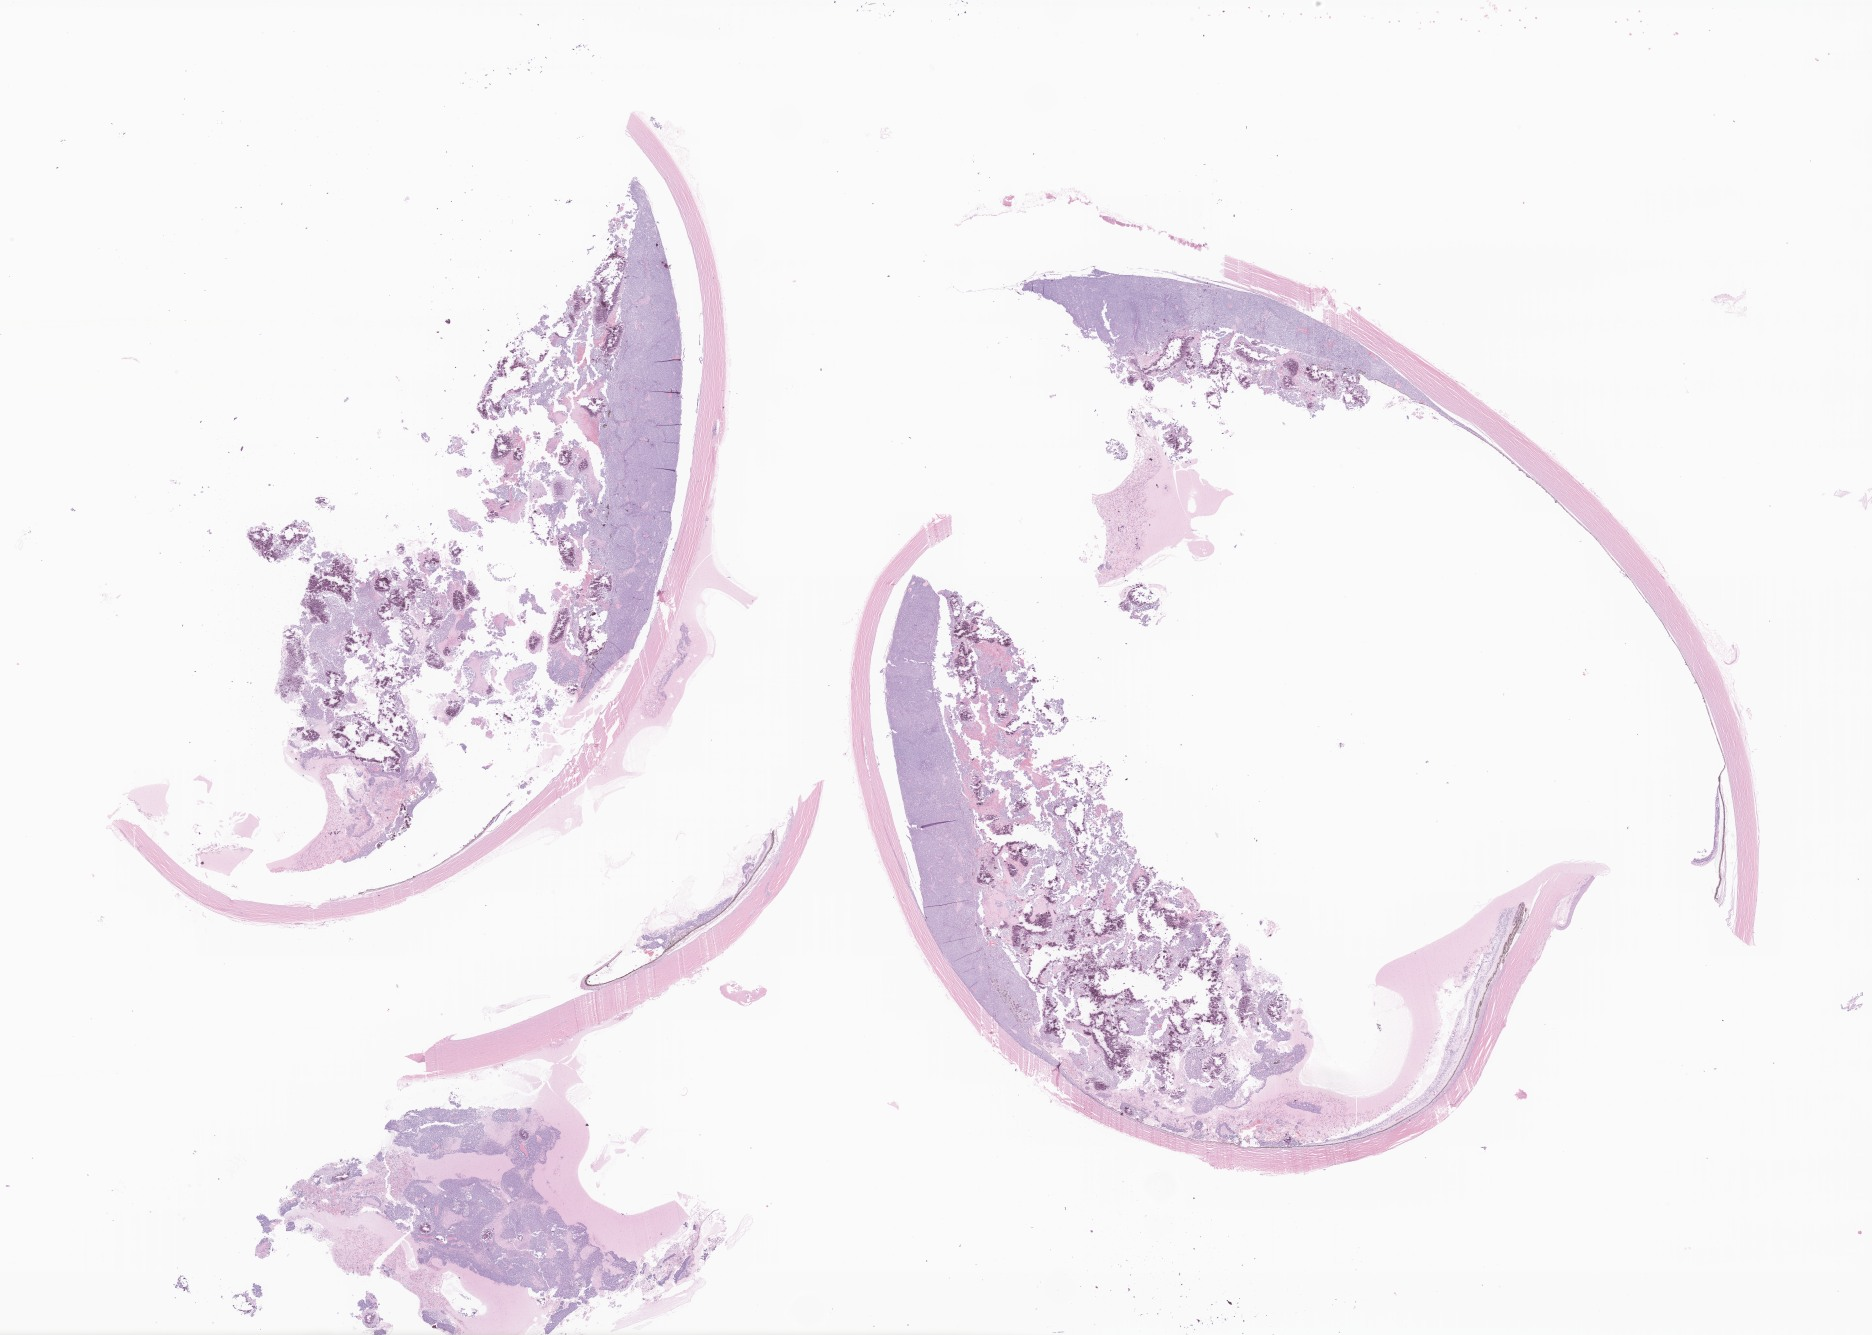
Haematoxylin and eosin whole-slide image of tumor tissue from the eye — shown as a low-resolution overview of the whole scanned area (about 31.6 x 22.5 mm). FFPE section. Male patient, age 342 days.
* diagnosis: Retinoblastoma, NOS